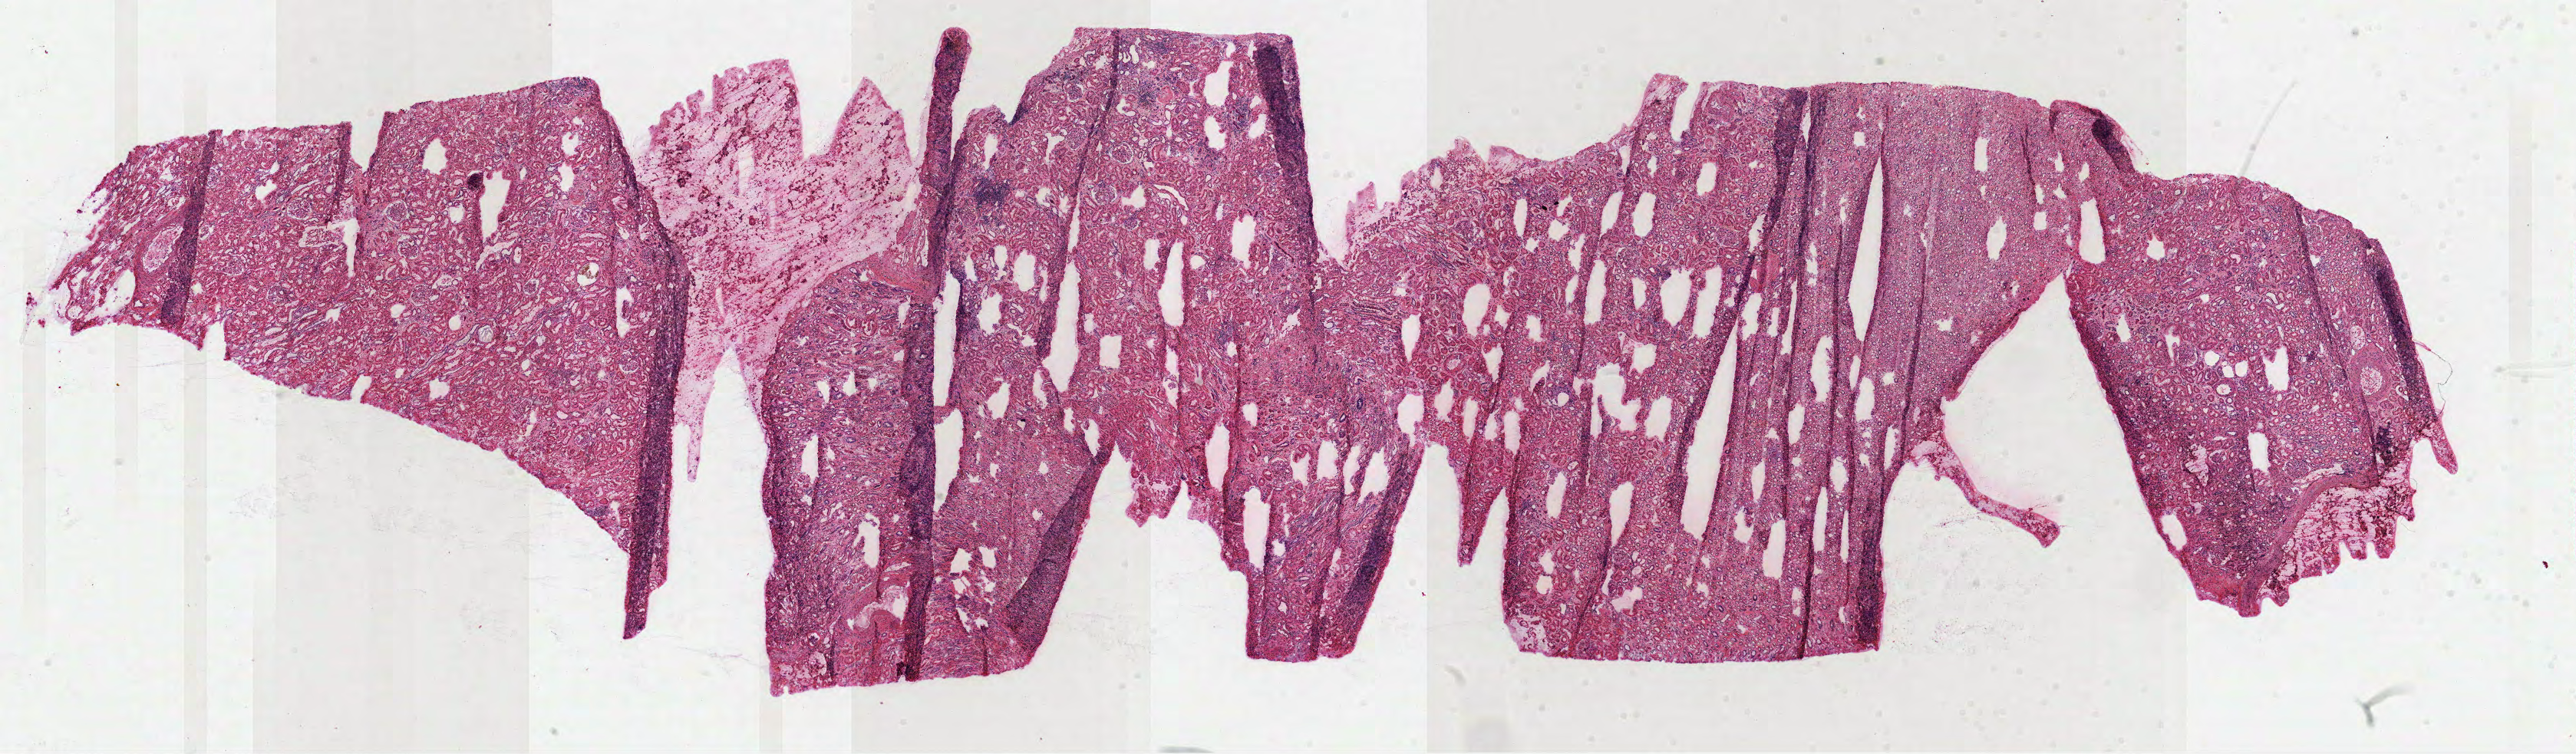
H&E whole-slide image — shown as a low-resolution overview of the whole scanned area (about 27.1 x 7.9 mm), frozen section from the top of the tissue portion, kidney, solid tissue normal (non-tumour tissue) sample. Male patient; age at initial diagnosis 65 years.
This section: solid tissue normal (non-tumour) sample from the same patient. Patient diagnosis: Clear cell adenocarcinoma, NOS.